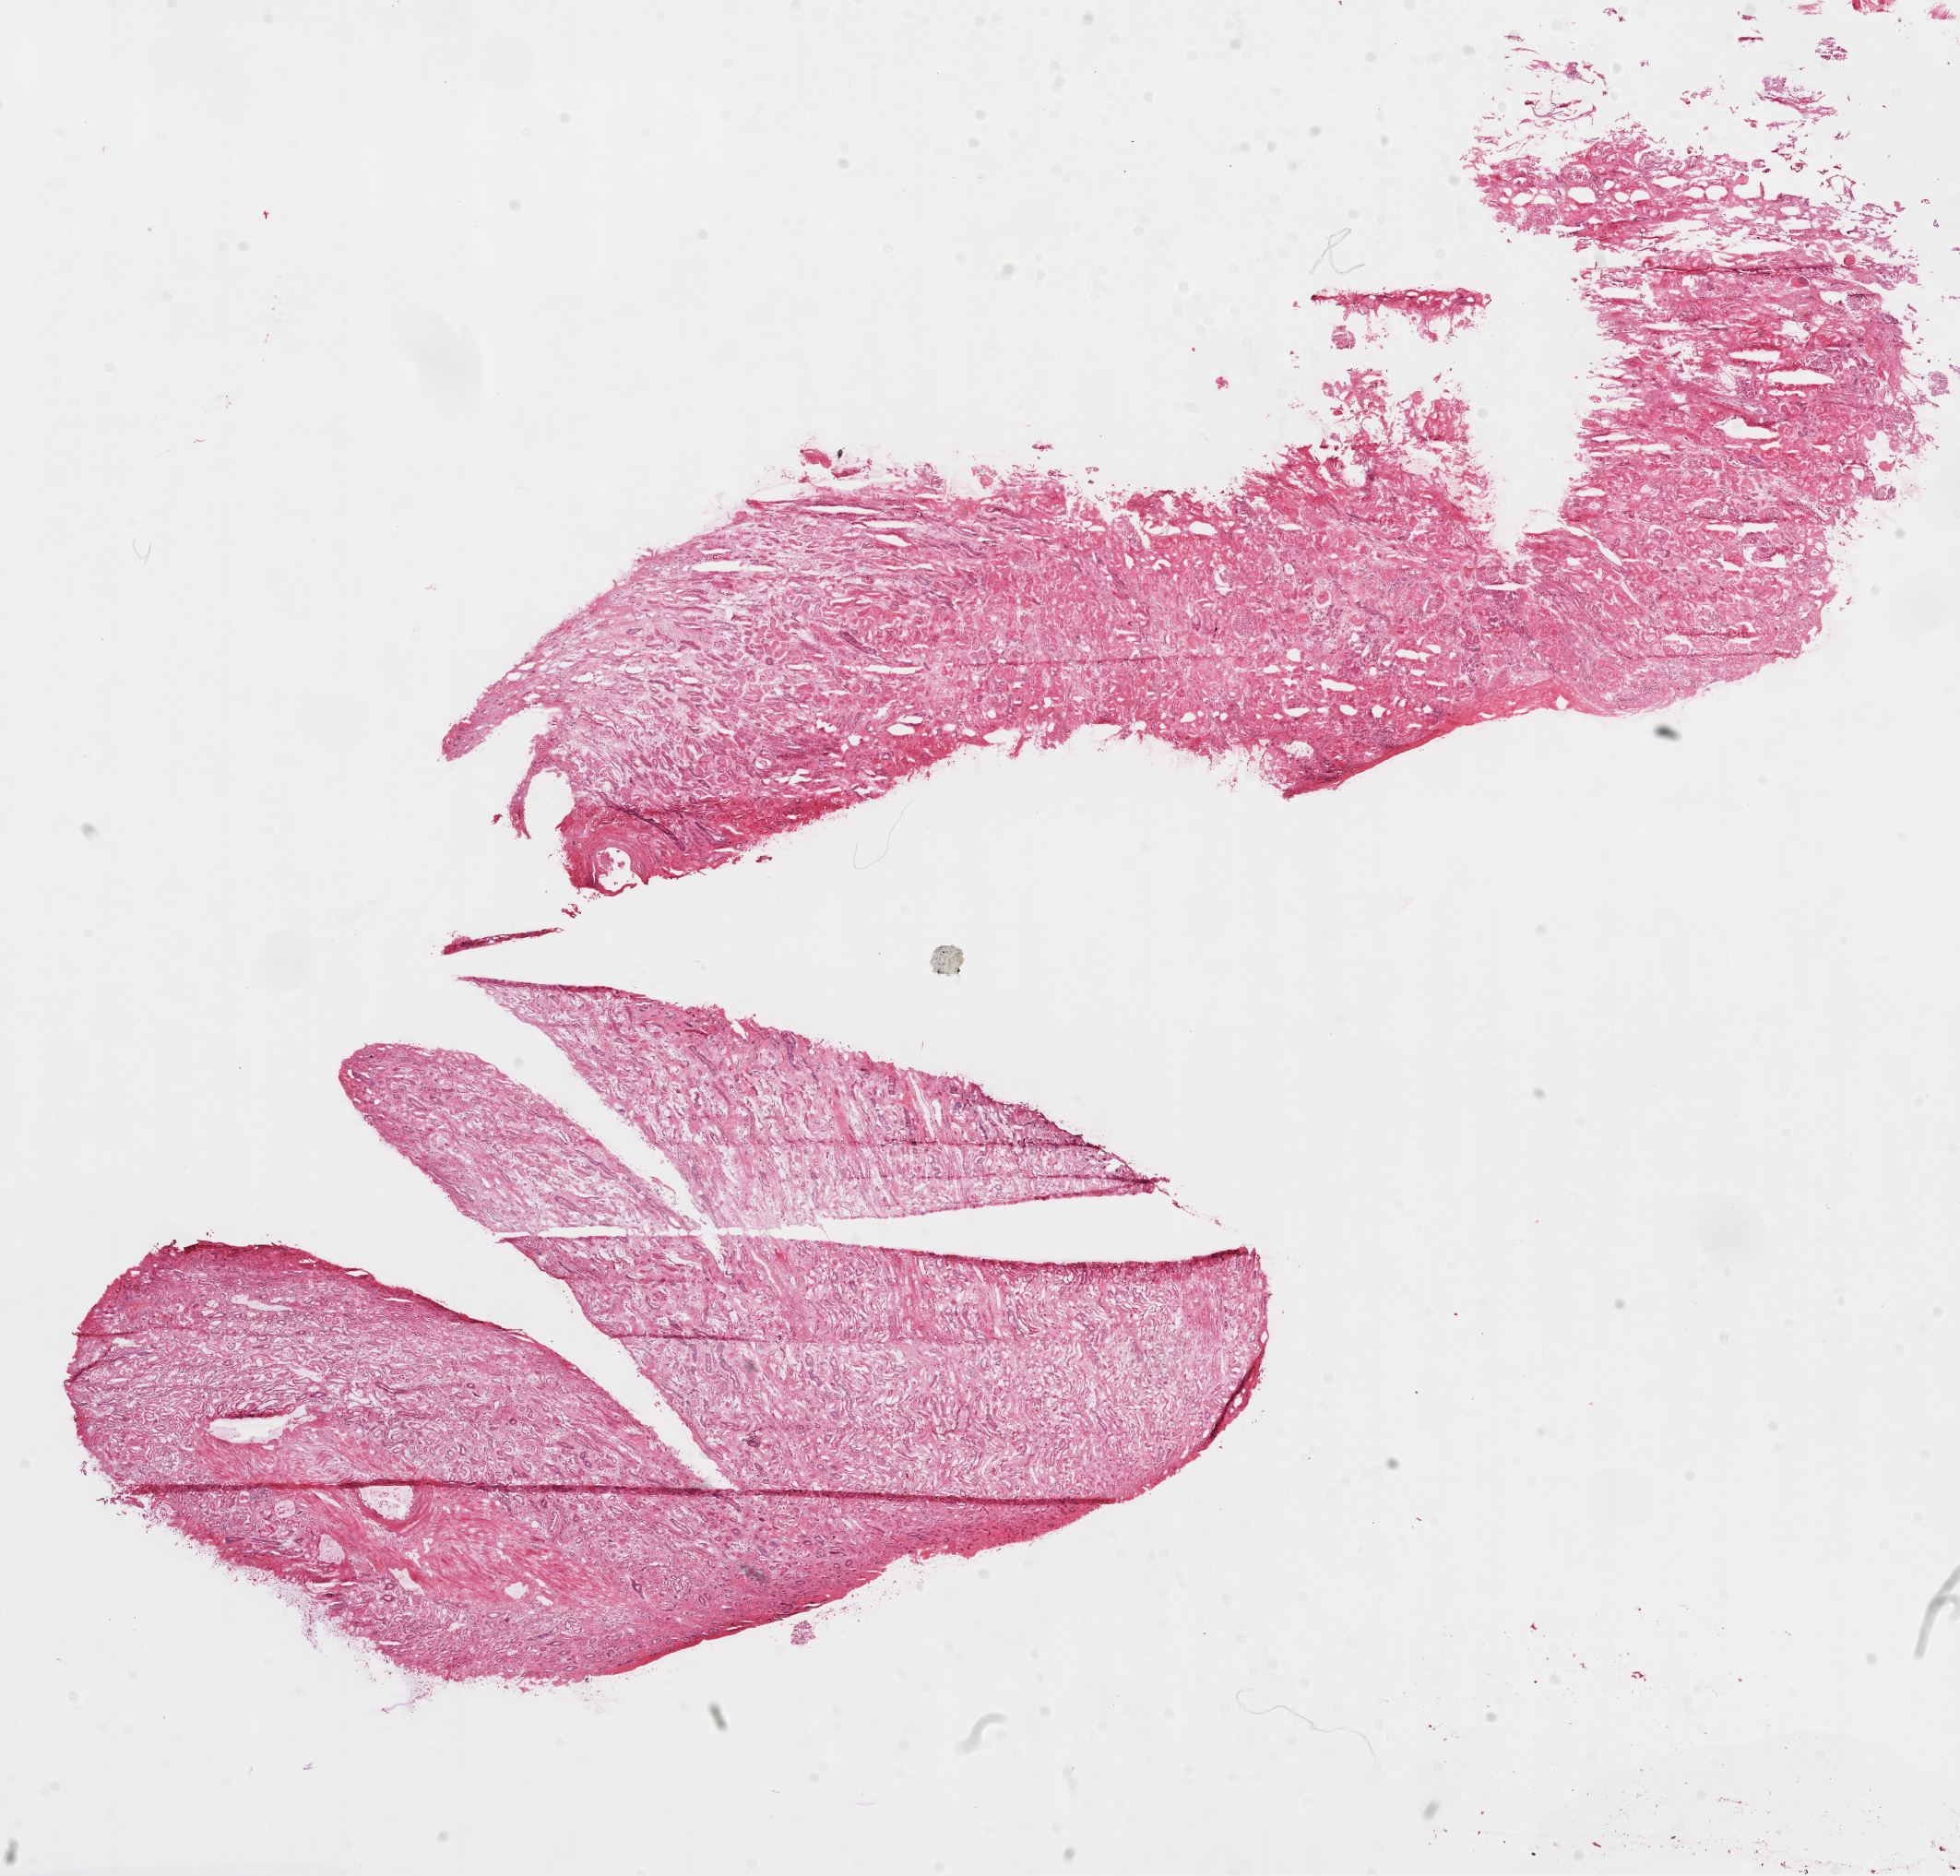
Hematoxylin and eosin (H&E) stained whole-slide image, shown as a low-resolution overview of the whole scanned area (about 17.1 x 16.3 mm, from a 20x scan), frozen section from the top of the tissue portion, solid tissue normal (non-tumour tissue) sample from the kidney. Patient: male, age at initial diagnosis 73 years.
- this section: solid tissue normal (non-tumour) sample from the same patient
- patient diagnosis: Clear cell adenocarcinoma, NOS